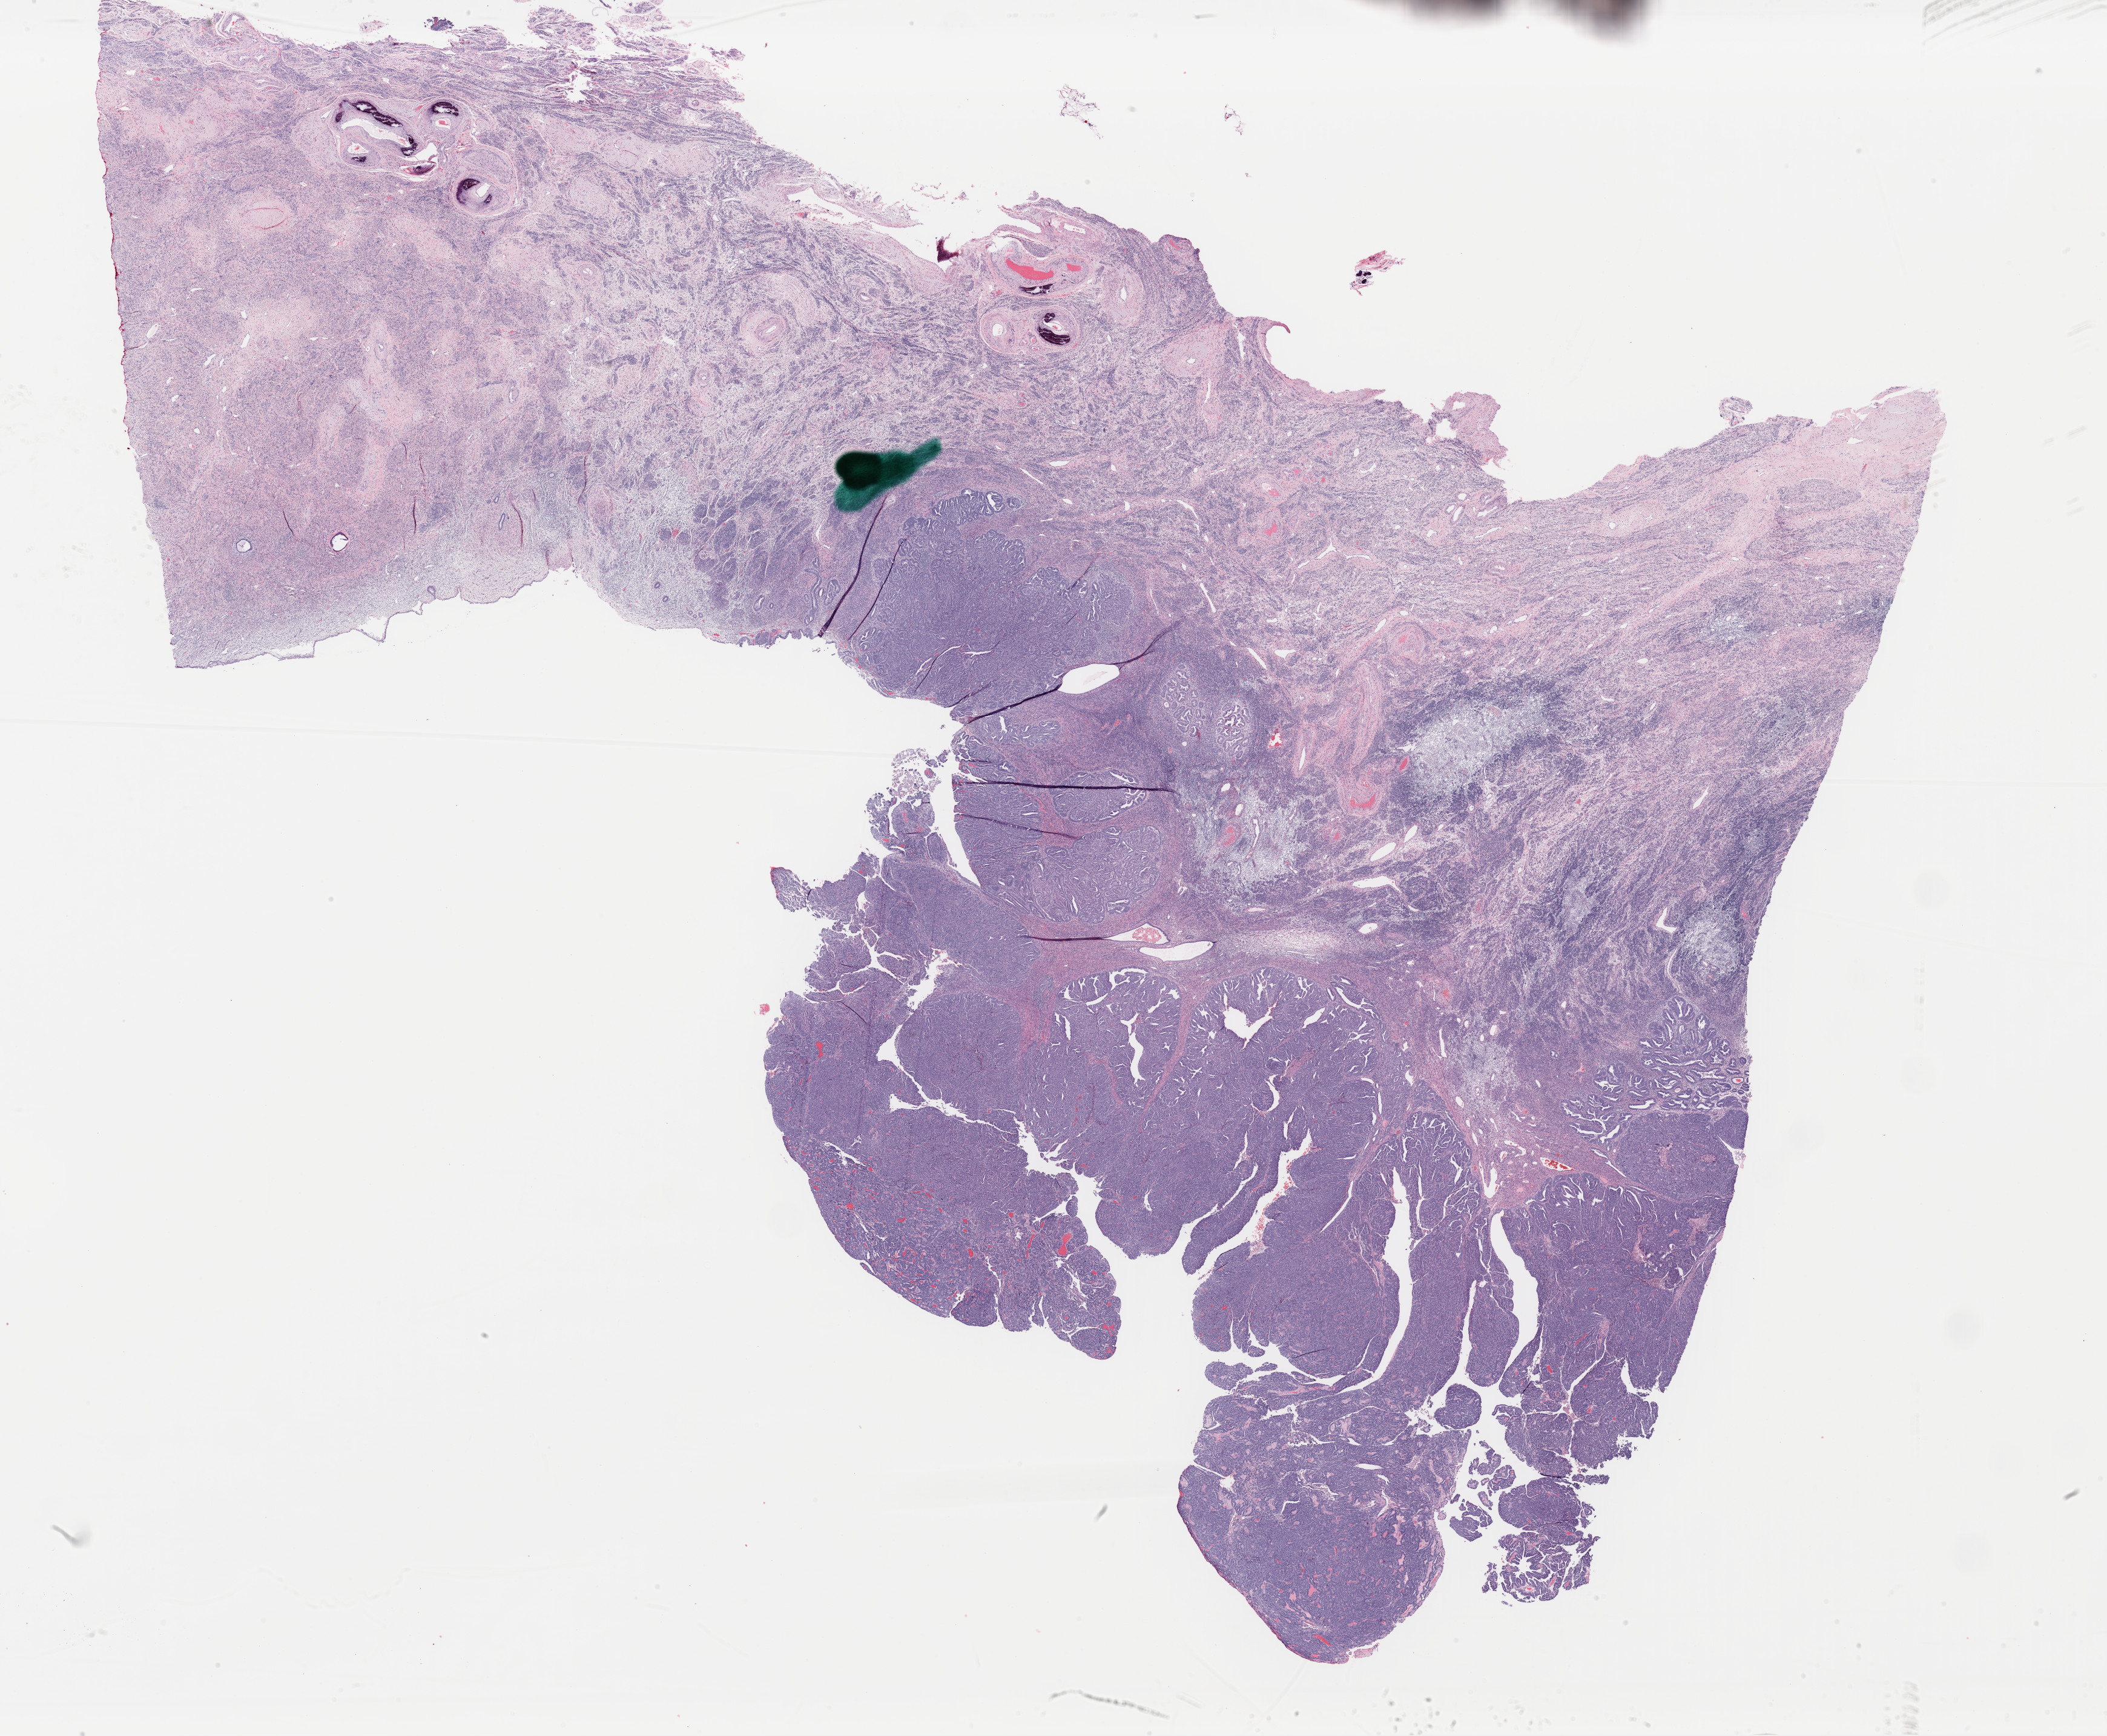
H&E whole-slide image, shown as a low-resolution overview of the whole scanned area (about 27.5 x 22.7 mm, acquisition: 40x scan); FFPE section; primary tumour sample from the uterus. Female, age 77 years at initial diagnosis. Histologic grade: G3 (poorly differentiated).
FIGO stage: IB. Lymph nodes positive (case pathology): 0 of 24 examined. Pathologic diagnosis: Serous cystadenocarcinoma, NOS (endometrium).